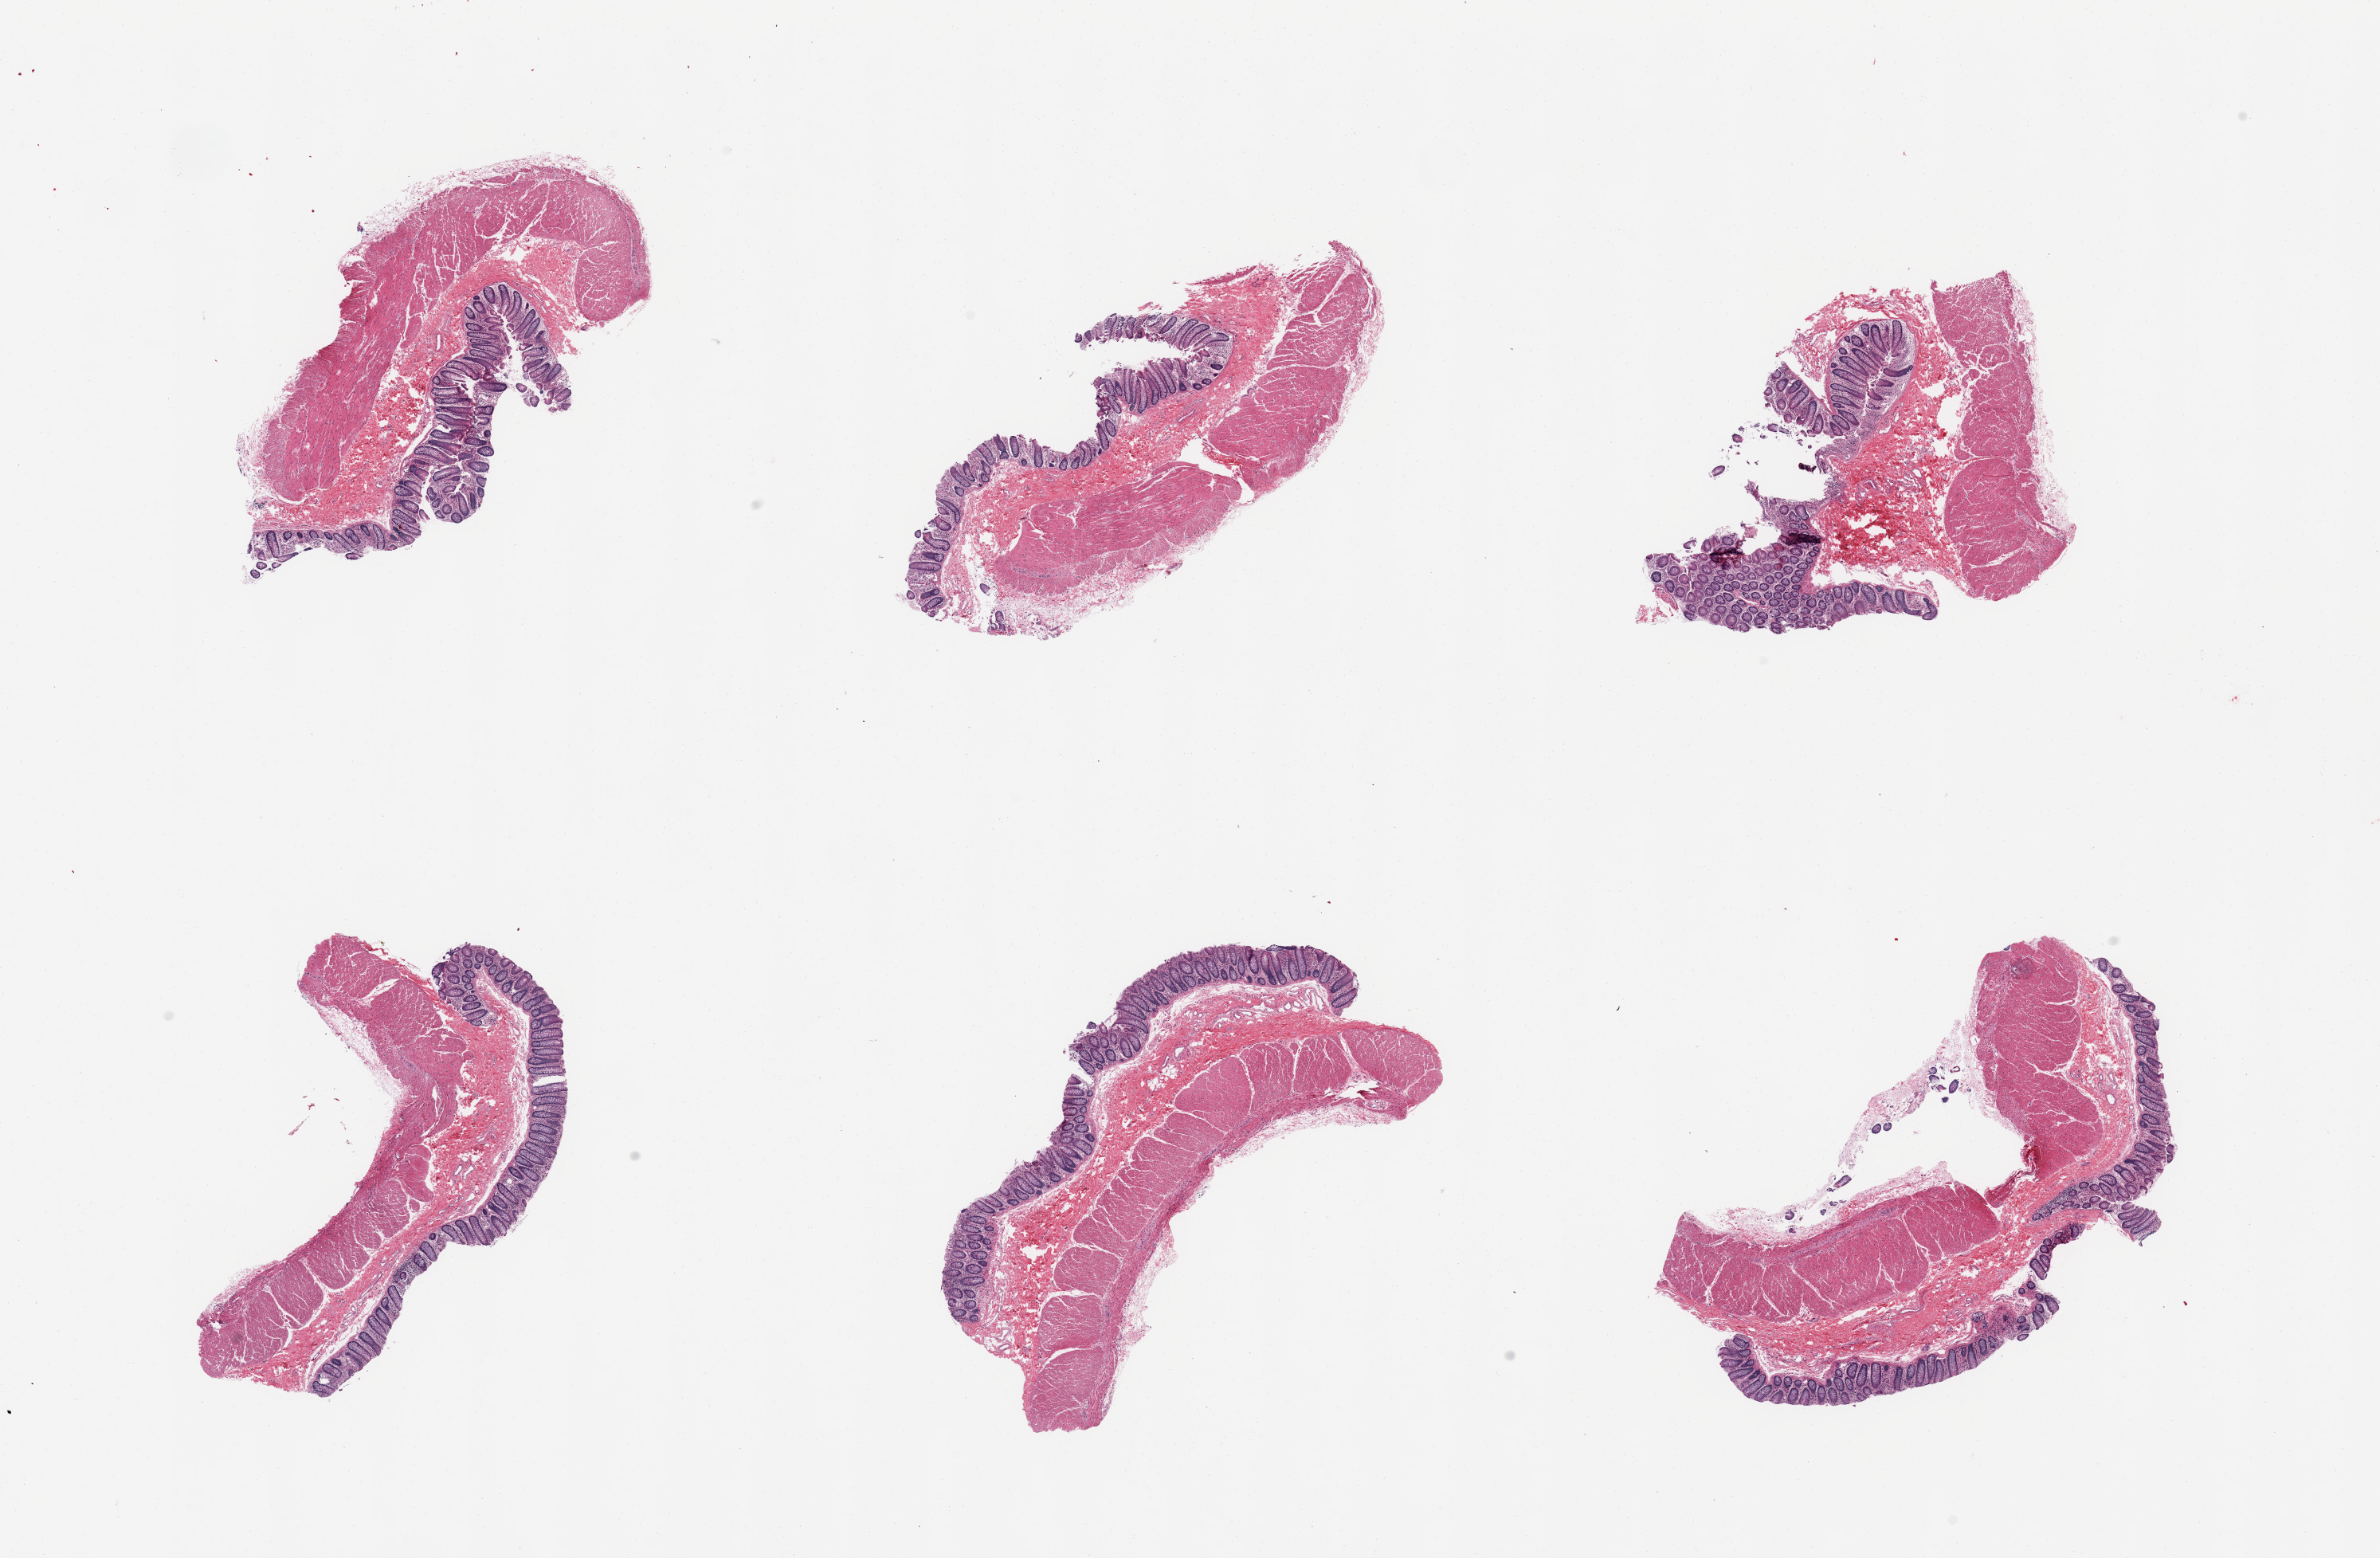
Haematoxylin and eosin whole-slide image, shown as a low-resolution overview of the whole scanned area (about 23.6 x 15.5 mm, slide scanned at 20x); PAXgene-fixed paraffin-embedded (PFPE) section; section of transverse colon (target tissue); tissue donor sample. Donor: female.
• reviewer comment on this tissue sample: 6 pieces; all full thickness; well preserved